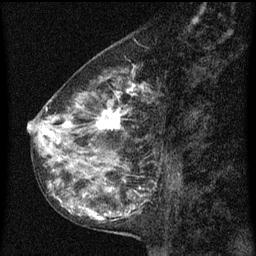
Breast MRI (dynamic contrast-enhanced), one sagittal slice; dynamic contrast-enhanced series, image 2 of 3 at this slice position (ordered by acquisition); 1.5 T; TE 4.2 ms, TR 8 ms; 2 mm slice thickness; 256 × 256 image matrix, field of view 180 × 180 mm. Female patient, age 55 years.
Outlined on this slice (semi-automatically segmented with operator editing):
- analysis volume of interest (the breast-tissue region the enhancement analysis was run in; not a lesion): bounding box [x1, y1, x2, y2] px = [34, 70, 159, 151]
- tumour enhancement mask (voxels above the 70 % enhancement threshold inside the analysis volume of interest): [38, 80, 147, 145]